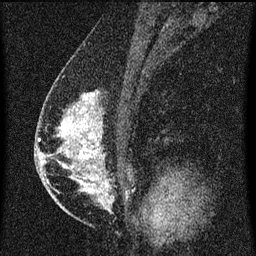
Breast MRI (dynamic contrast-enhanced), one sagittal slice; position 35 of 60 along the scan axis; dynamic contrast-enhanced series, image 2 of 3 at this slice position (ordered by acquisition); 1.5 T; TE 4.2 ms, TR 8 ms; 256 × 256 image matrix. Patient: female, 47 years.
Annotated regions visible in this slice (semi-automatically segmented with operator editing):
- analysis volume of interest (the breast-tissue region the enhancement analysis was run in; not a lesion): box from (x=50, y=80) to (x=128, y=203) px
- tumour enhancement mask (voxels above the 70 % enhancement threshold inside the analysis volume of interest): (x=62, y=94)–(x=108, y=193)